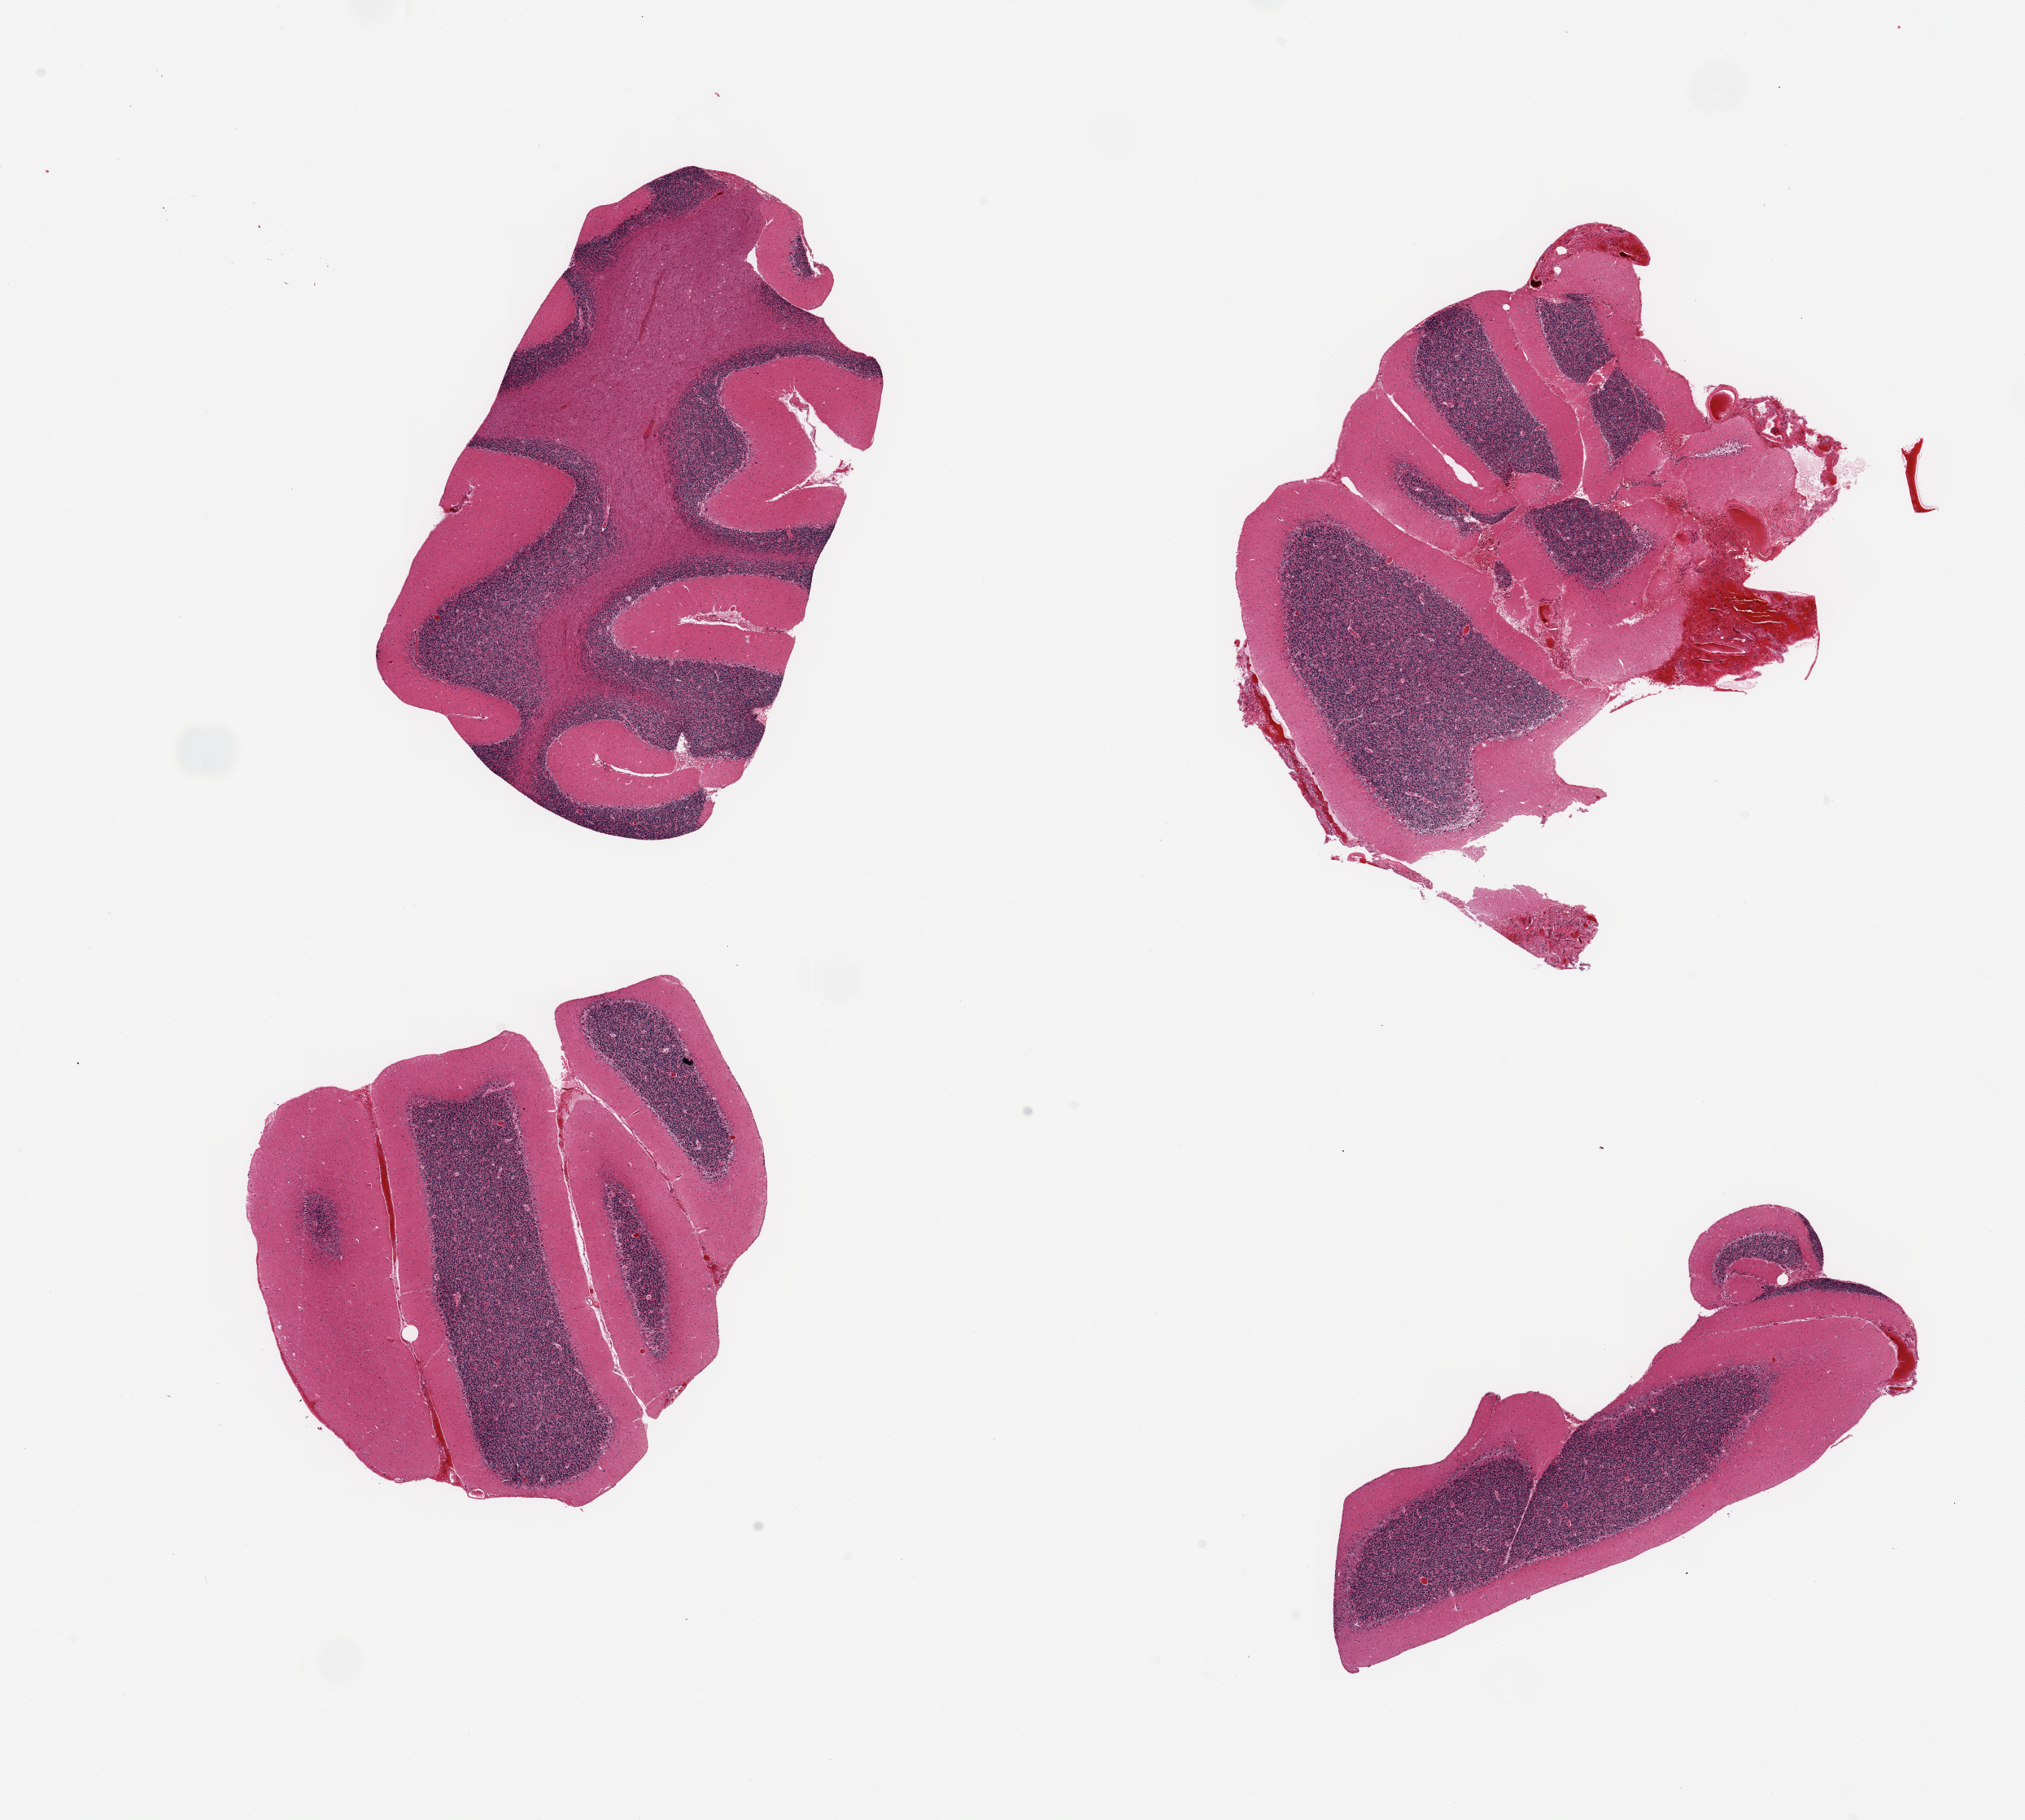
Whole-slide image, haematoxylin and eosin stain, whole scanned area (about 19.7 x 17.7 mm, slide scanned at 20x) shown as a low-resolution overview. PAXgene-fixed paraffin-embedded (PFPE) section. Target tissue: cerebellum. Donor tissue sample. Donor: female.
• review note (as recorded): 4 pieces